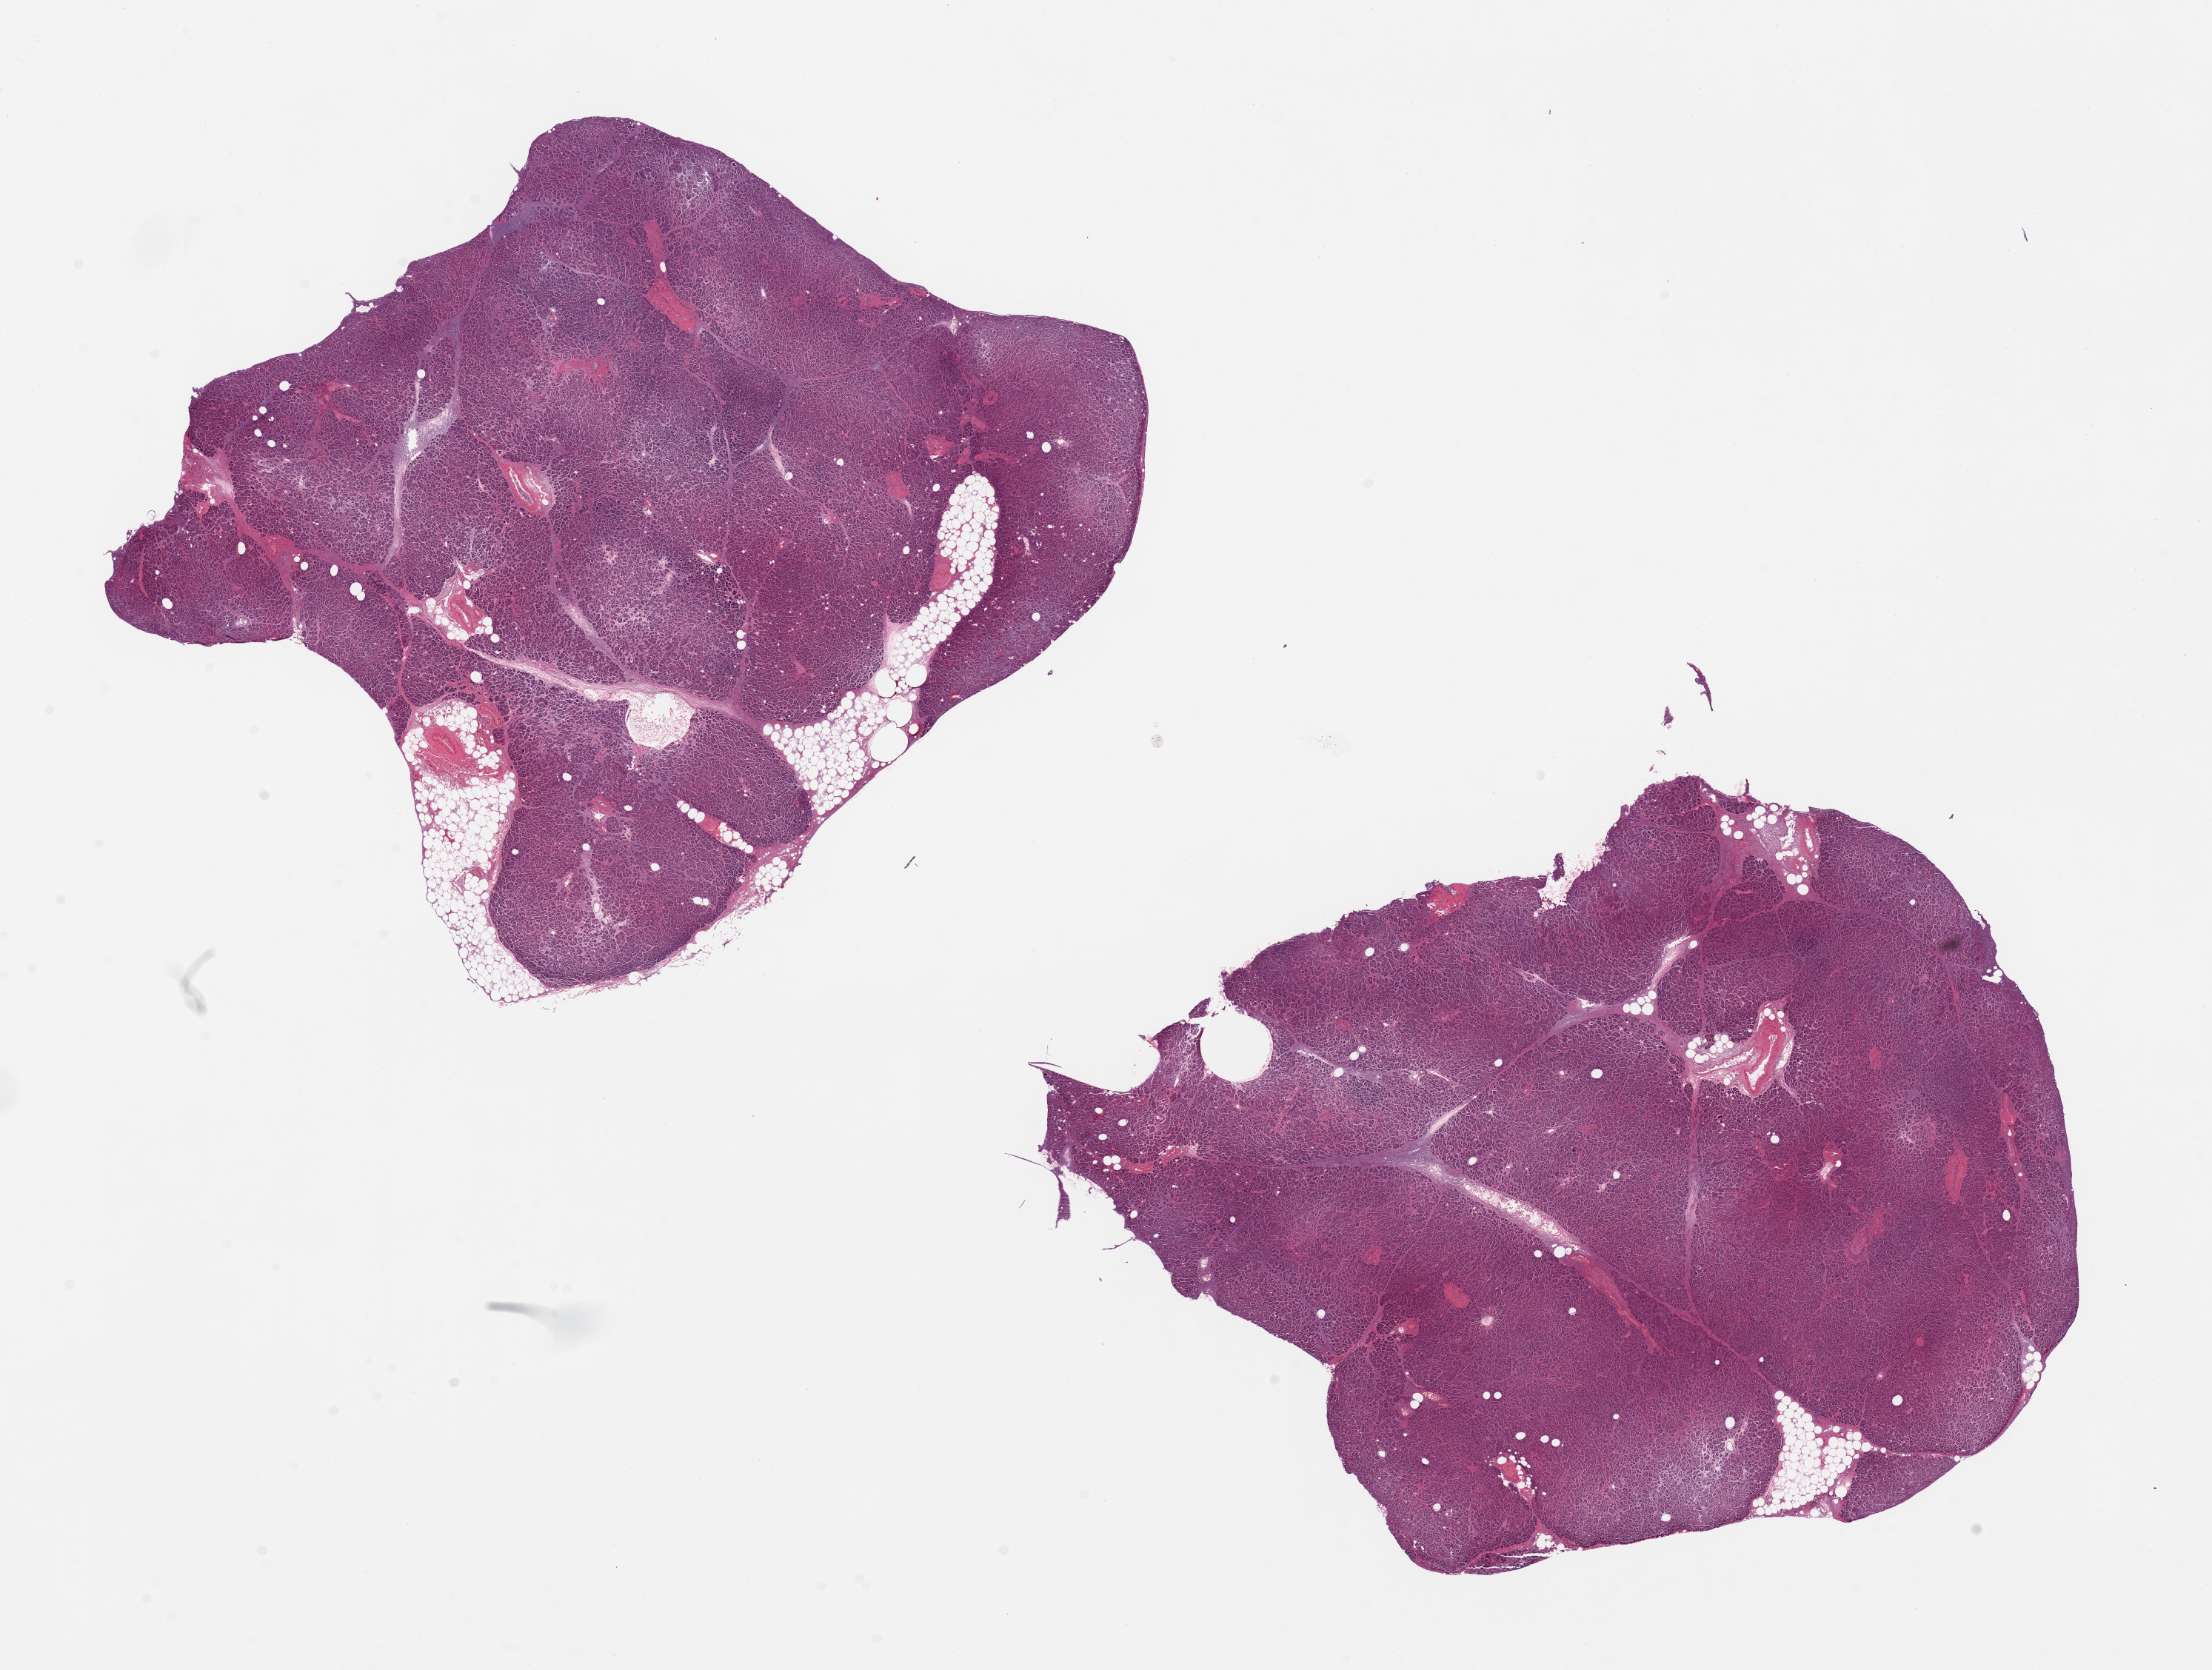
Digitized hematoxylin and eosin (H&E)-stained section, brightfield, shown as a low-resolution overview of the whole scanned area (about 23.6 x 17.8 mm, acquisition: 20x scan), PAXgene-fixed paraffin-embedded (PFPE) section, section of pancreas (target tissue), tissue donor sample. Donor: male.
- reviewer comment on this tissue sample: 2 pieces; 5 & 10% internal fat